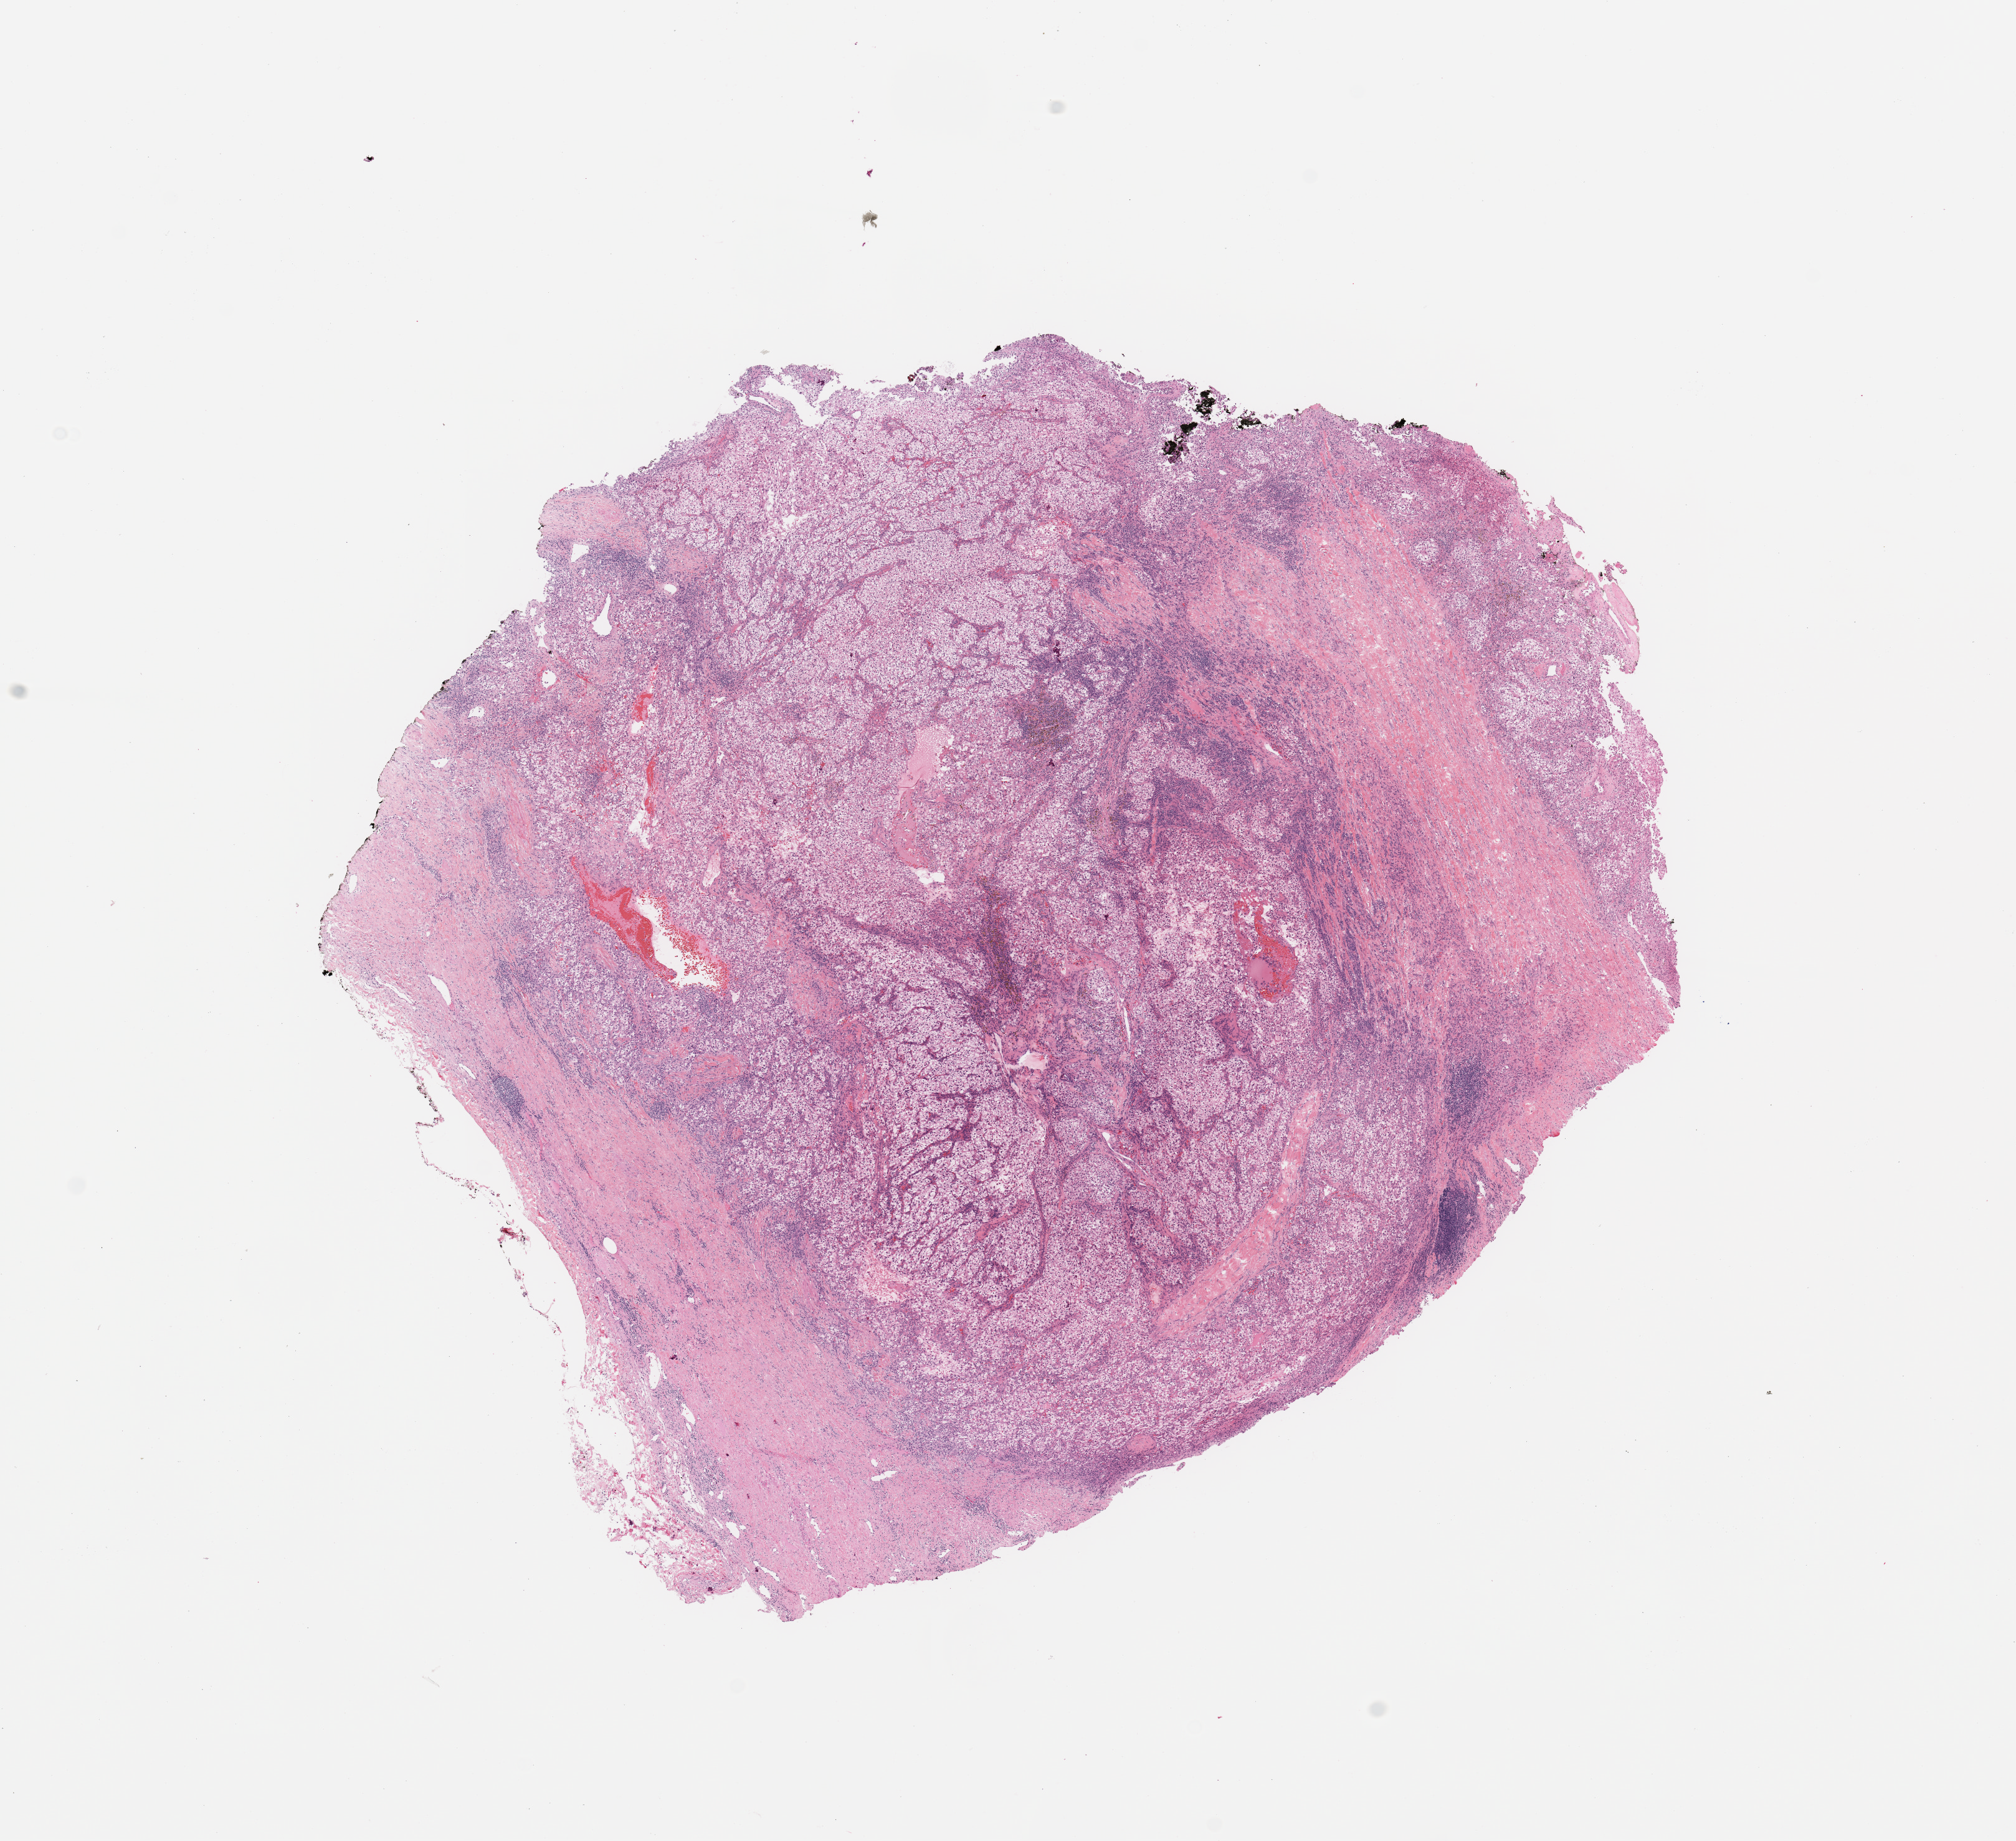
Whole-slide histology image, H&E-stained — a low-resolution overview of the entire scanned area, about 12.8 x 11.7 mm (slide scanned at 20x); tumour tissue sample, kidney. Male, 43 y/o. Histologic grade: G2 (moderately differentiated).
AJCC pathologic stage: I. Diagnosis: Renal cell carcinoma, NOS.